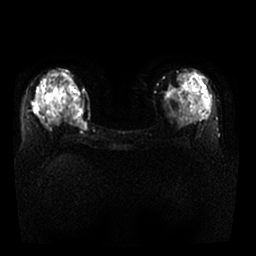
Breast MRI, one axial slice; slice 16 of 29 in the series (ordered by position); diffusion-weighted series; image 2 of 4 stored at this slice position (different b-values; order by instance number); 1.5 T; 256 × 256 image matrix, field of view 340 × 340 mm. Female patient.
Structures marked on this image (manually delineated by an expert):
- tumour on diffusion-weighted imaging: bounding box (x1, y1, x2, y2) in pixels: (75, 106, 87, 131)